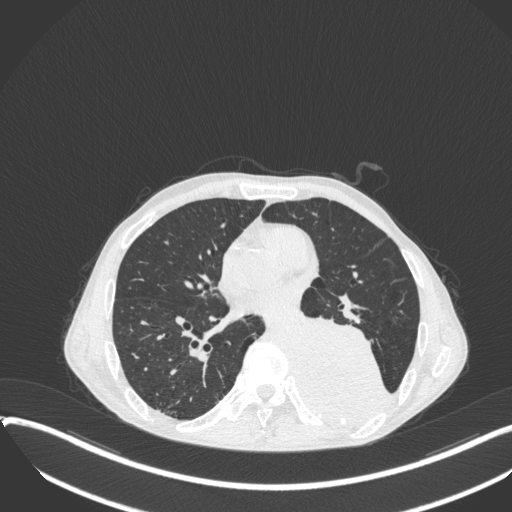
Chest CT, one axial slice. Slice 166 of 400 in the series (ordered by position). Reconstruction kernel B31f. 120 kVp. Lung window (W 1500 / L -600 HU). 512 × 512 image matrix, field of view 400 × 400 mm. Patient: male, 57 years. From the clinical record (not read from this slice): clinical TNM (as recorded): T4 N0 M0.
Outlined on this slice (bounding box drawn by a radiologist):
- lung tumour (recorded histology: squamous cell carcinoma): bounding box (x1, y1, x2, y2) in pixels: (295, 303, 396, 427)